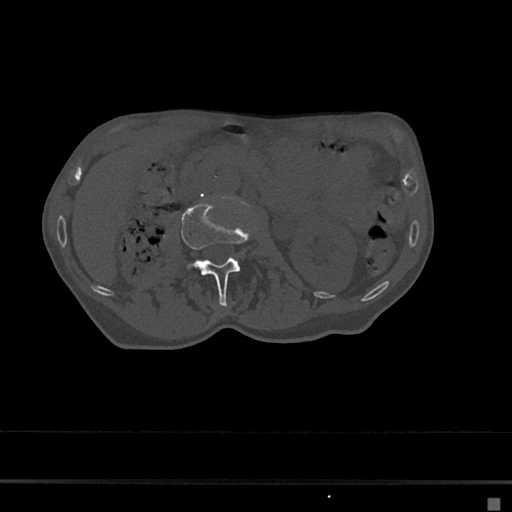
CT including the spine, one axial slice; slice 6 of 797 in the series (ordered by position); reconstruction kernel Br40s/3; 120 kVp; bone window (W 1800 / L 400 HU); 0.5 mm slice thickness; 512 × 512 image matrix. Patient: female, 68 years. From the clinical record (not read from this slice): primary cancer: renal.
Structures marked on this image (semi-automatic segmentation, software-assisted and operator-edited):
- L2 vertebra: bounding box [x1, y1, x2, y2] px = [181, 201, 255, 305]